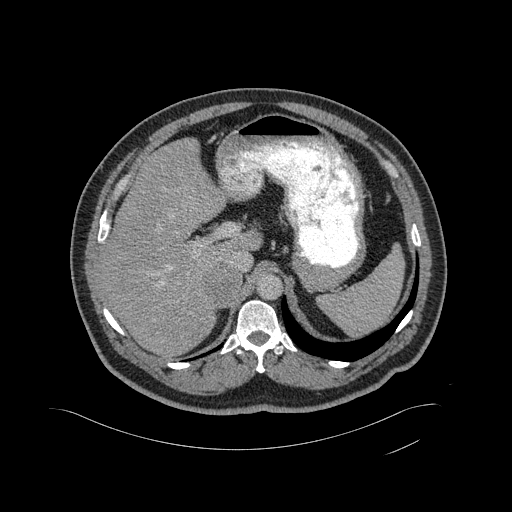
Contrast-enhanced abdominal CT, one axial slice; slice 334 of 433 in the series (ordered by position); 120 kVp; soft-tissue window (W 400 / L 40 HU); 2 mm slice thickness; 512 × 512 image matrix, field of view 500 × 500 mm. Patient: male, 56 years. From the clinical record (not read from this slice): diagnosis: adrenocortical carcinoma; tumour side: right adrenal; tumour size at pathology: 11.6 cm; Ki-67 index: 50 %; stage (as recorded): 3.
Outlined on this slice (semi-automatic segmentation, software-assisted and operator-edited):
- mass: bounding box (x1, y1, x2, y2) in pixels: (204, 265, 242, 305)